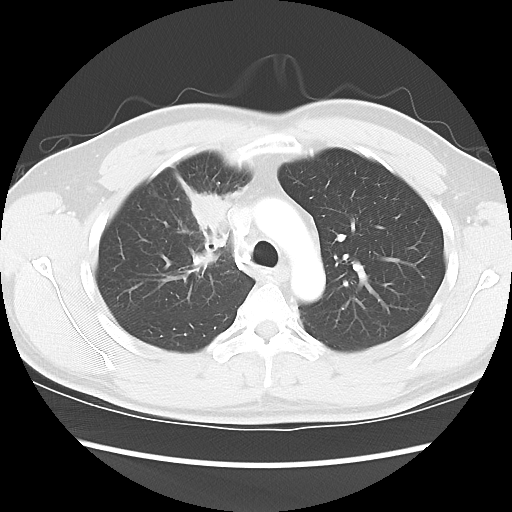
Chest CT, one axial slice; slice 64 of 80 in the series (ordered by position); reconstruction kernel LUNG; lung window (W 1500 / L -600 HU); 512 × 512 image matrix, field of view 360 × 360 mm. Male patient, age 35 years. Case-level facts recorded for this patient, not image findings: clinical TNM (as recorded): T1c N1 M1b.
Outlined on this slice (bounding box drawn by a radiologist):
- lung tumour (recorded histology: adenocarcinoma): bounding box [x1, y1, x2, y2] px = [187, 185, 231, 236]